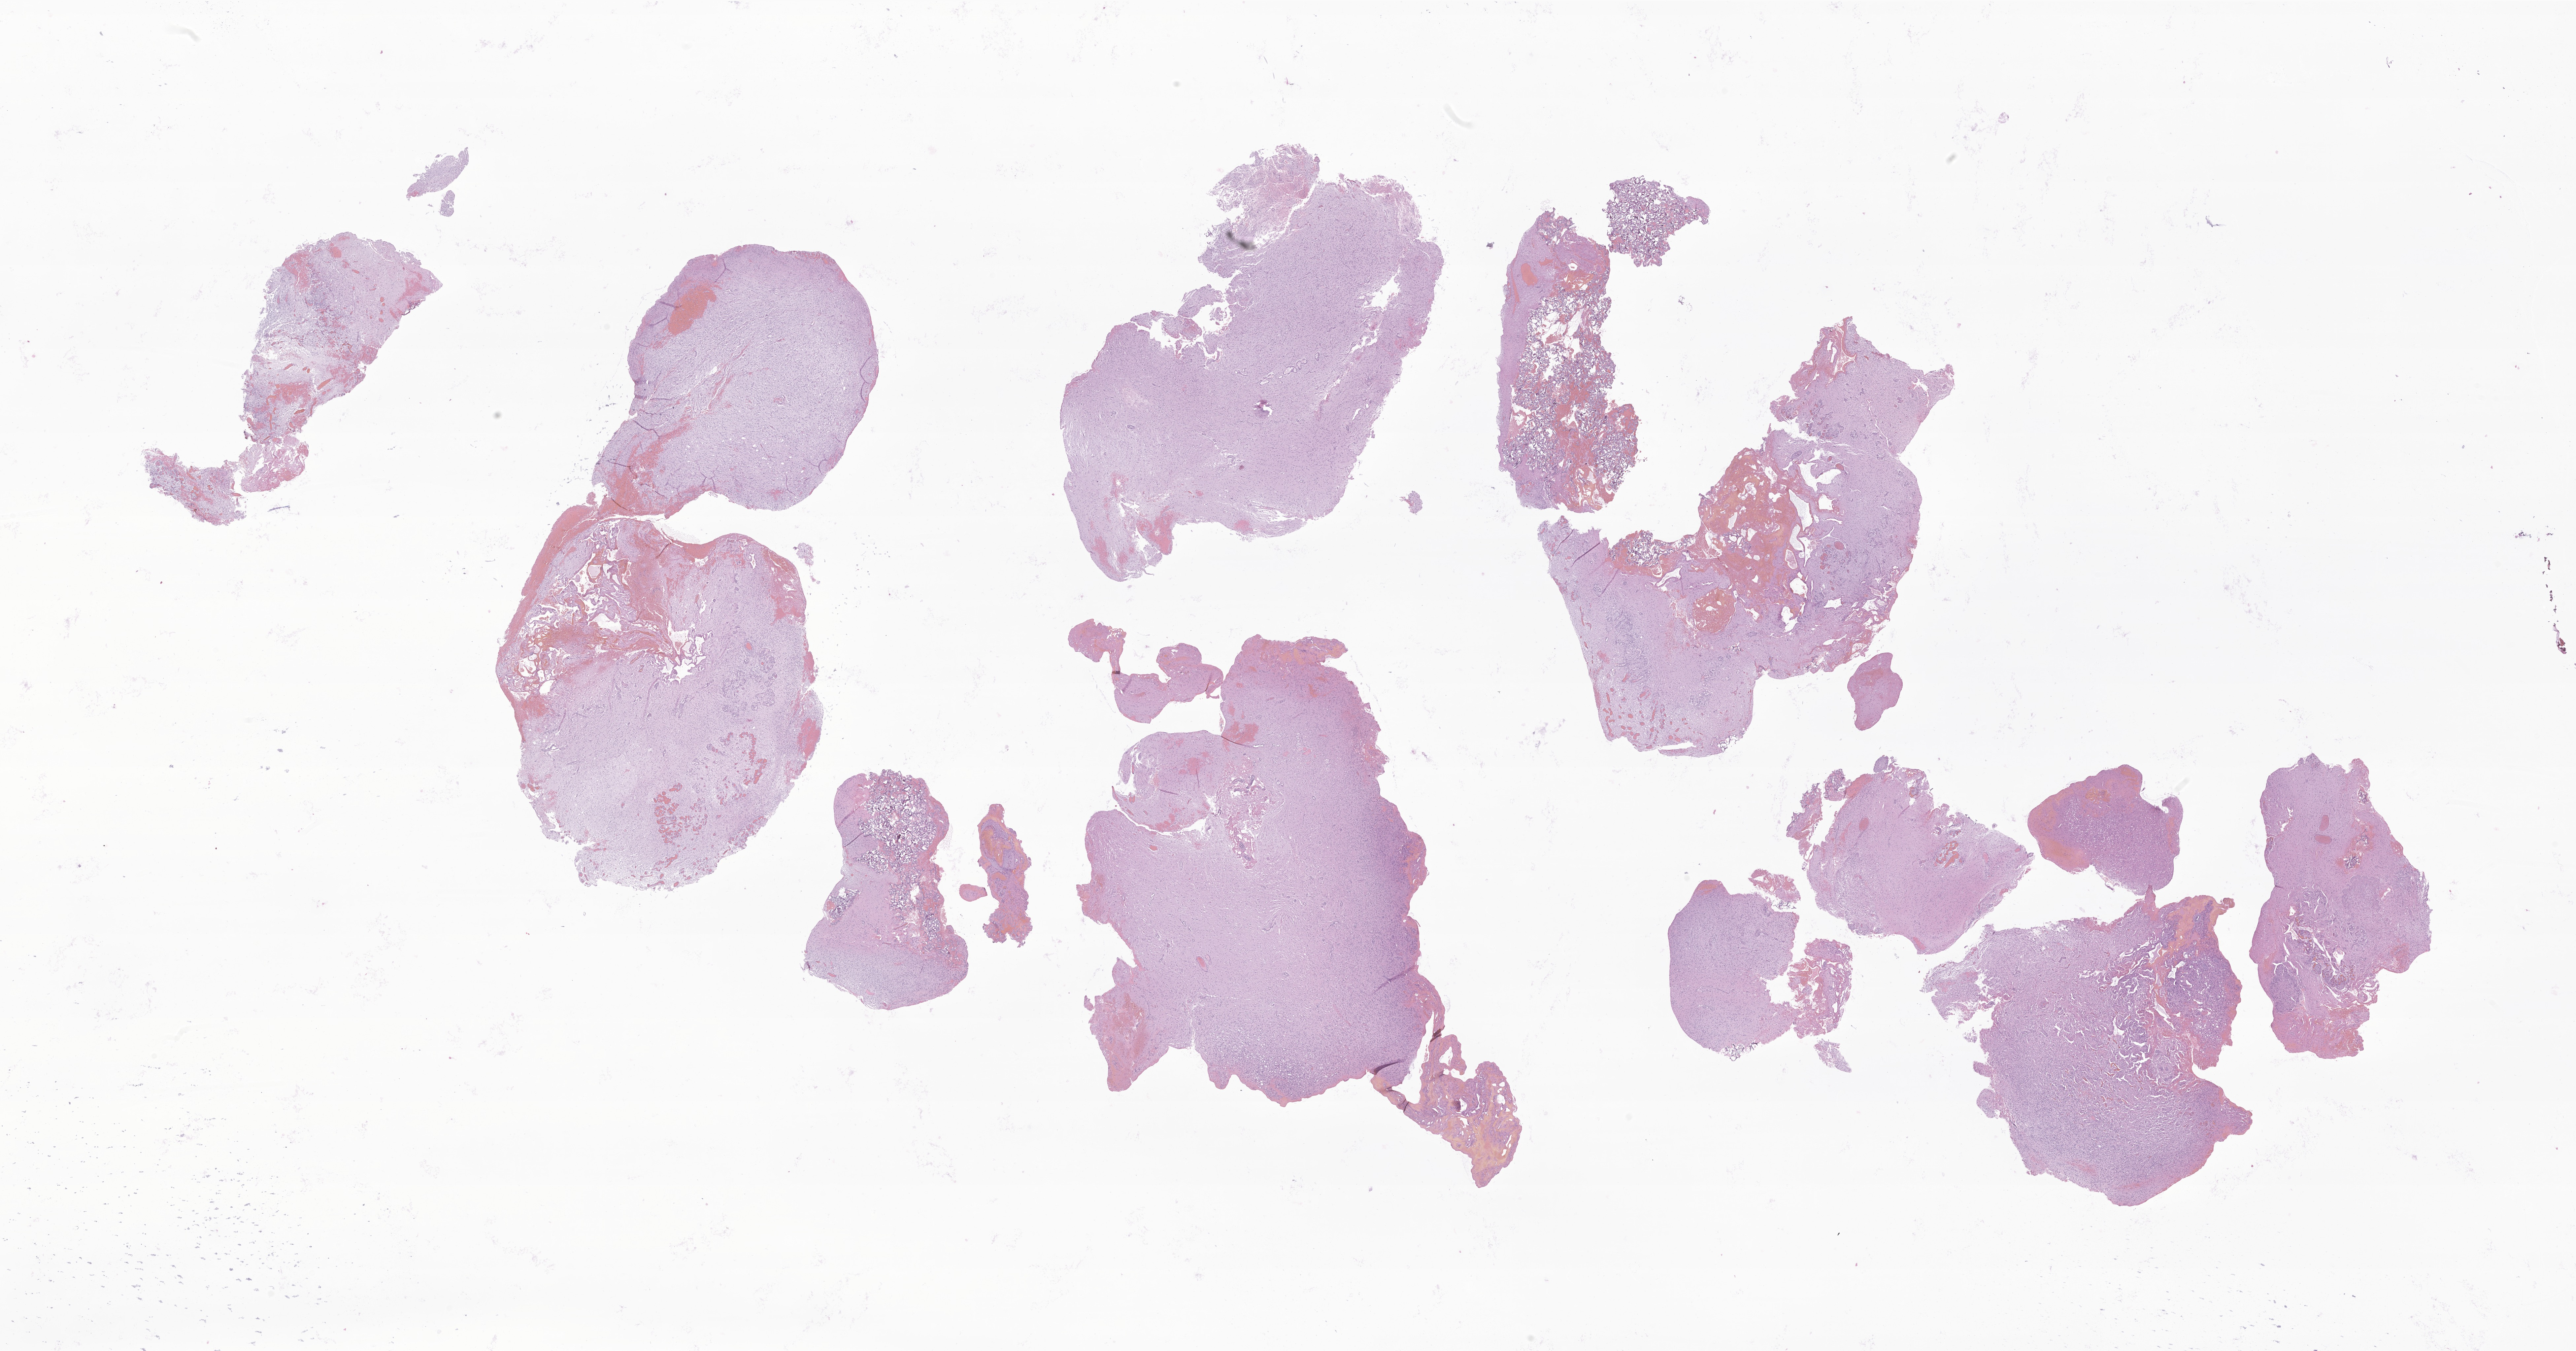
Whole-slide image, H&E stain of tumor tissue from the spinal cord, shown as a low-resolution overview of the whole scanned area (about 32.9 x 17.3 mm); FFPE section. Patient female; age 802 days.
Diagnosis: Astrocytoma, NOS.